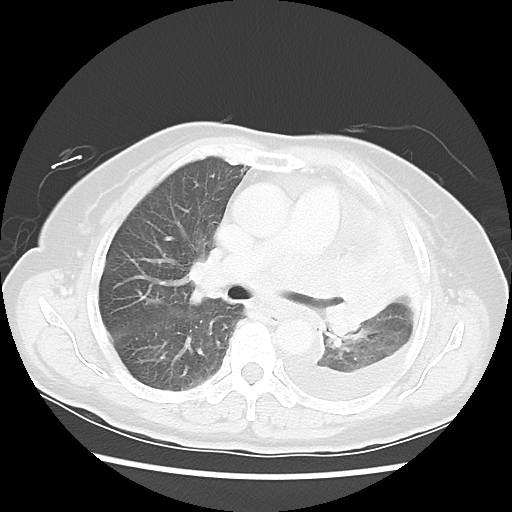
Chest CT, one axial slice. Slice 33 of 52 in the series (ordered by position). Reconstruction kernel LUNG. 120 kVp. Lung window (W 1500 / L -600 HU). 5 mm slice thickness. 512 × 512 image matrix, field of view 336 × 336 mm. Patient: female, 72 years. From the clinical record (not read from this slice): clinical TNM (as recorded): T4 N3 M1b.
Annotated regions visible in this slice (rectangle marked by the reading radiologist):
- lung tumour (recorded histology: large cell carcinoma): bounding box <307,246,404,348> (left, top, right, bottom; pixels)